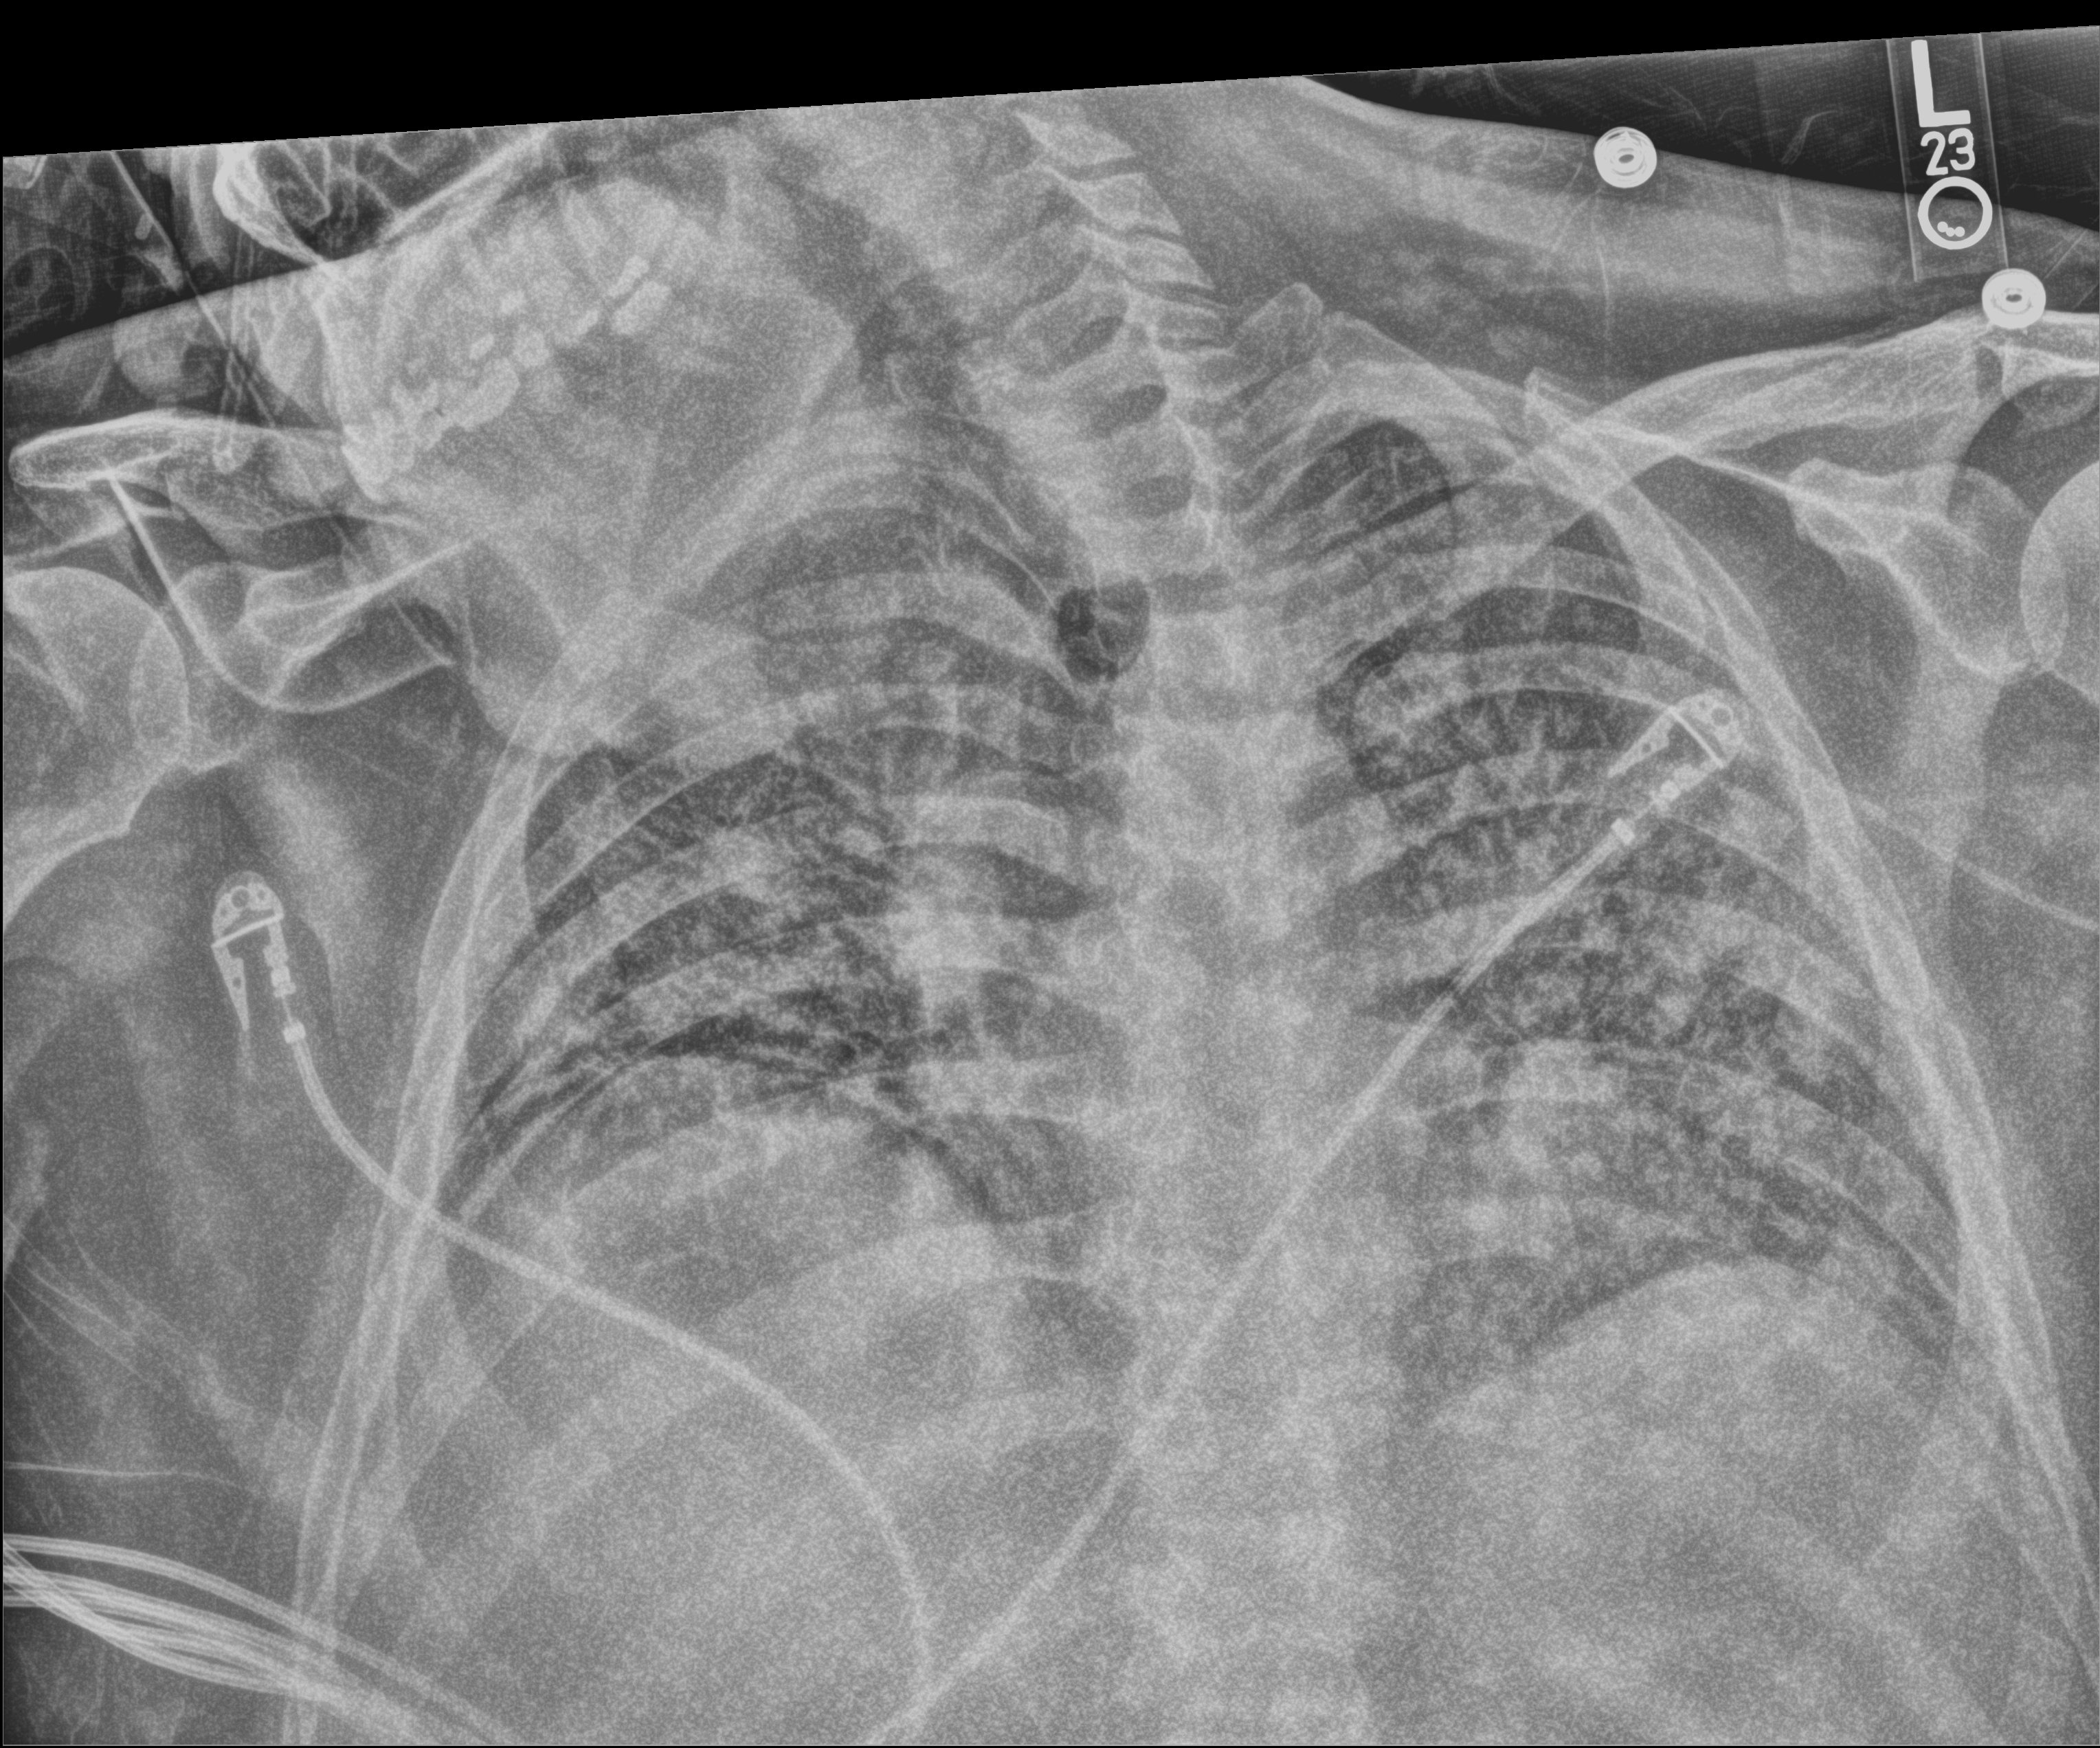
Portable chest radiograph; anteroposterior (AP) projection. Male patient hospitalised with COVID-19, age 18–59 years.
From the hospital-stay record, not from the radiograph (when in the stay this image was taken is not recorded): length of hospital stay: 80 days; mechanically ventilated during this hospital stay: yes; admitted to intensive care during this hospital stay: yes.